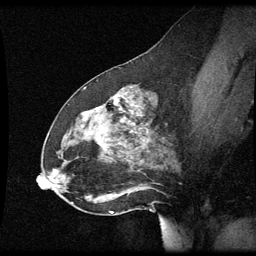
Breast MRI (dynamic contrast-enhanced), one sagittal slice; position 30 of 60 along the scan axis; dynamic contrast-enhanced series, image 2 of 3 at this slice position (ordered by acquisition); 1.5 T; TE 4.2 ms, TR 8.9 ms; 256 × 256 image matrix, field of view 200 × 200 mm. Patient: female, 49 years. Case-level facts recorded for this patient, not image findings: setting: breast cancer imaged before/during neoadjuvant chemotherapy; receptor status: HR-positive, HER2-negative.
Annotated regions visible in this slice (semi-automatic segmentation, software-assisted and operator-edited):
- analysis volume of interest (the breast-tissue region the enhancement analysis was run in; not a lesion): box from (x=46, y=92) to (x=174, y=205) px
- tumour enhancement mask (voxels above the 70 % enhancement threshold inside the analysis volume of interest): (x=115, y=98)–(x=122, y=111)